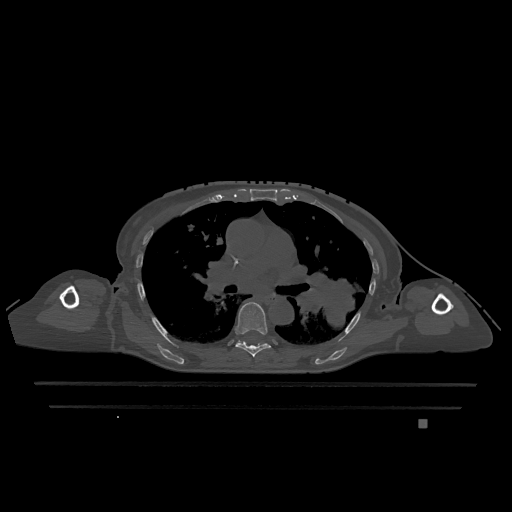
CT including the spine, one axial slice; slice 783 of 1317 in the series (ordered by position); bone window (W 1800 / L 400 HU); 512 × 512 image matrix, field of view 500 × 500 mm. Patient: female, 74 years. From the clinical record (not read from this slice): primary cancer: lung; vertebrae with lytic lesions (as recorded): T1, T4, T5, T6, L4, L5.
Annotated regions visible in this slice (semi-automatic segmentation, software-assisted and operator-edited):
- T6 vertebra: bounding box [x1, y1, x2, y2] px = [235, 302, 271, 357]